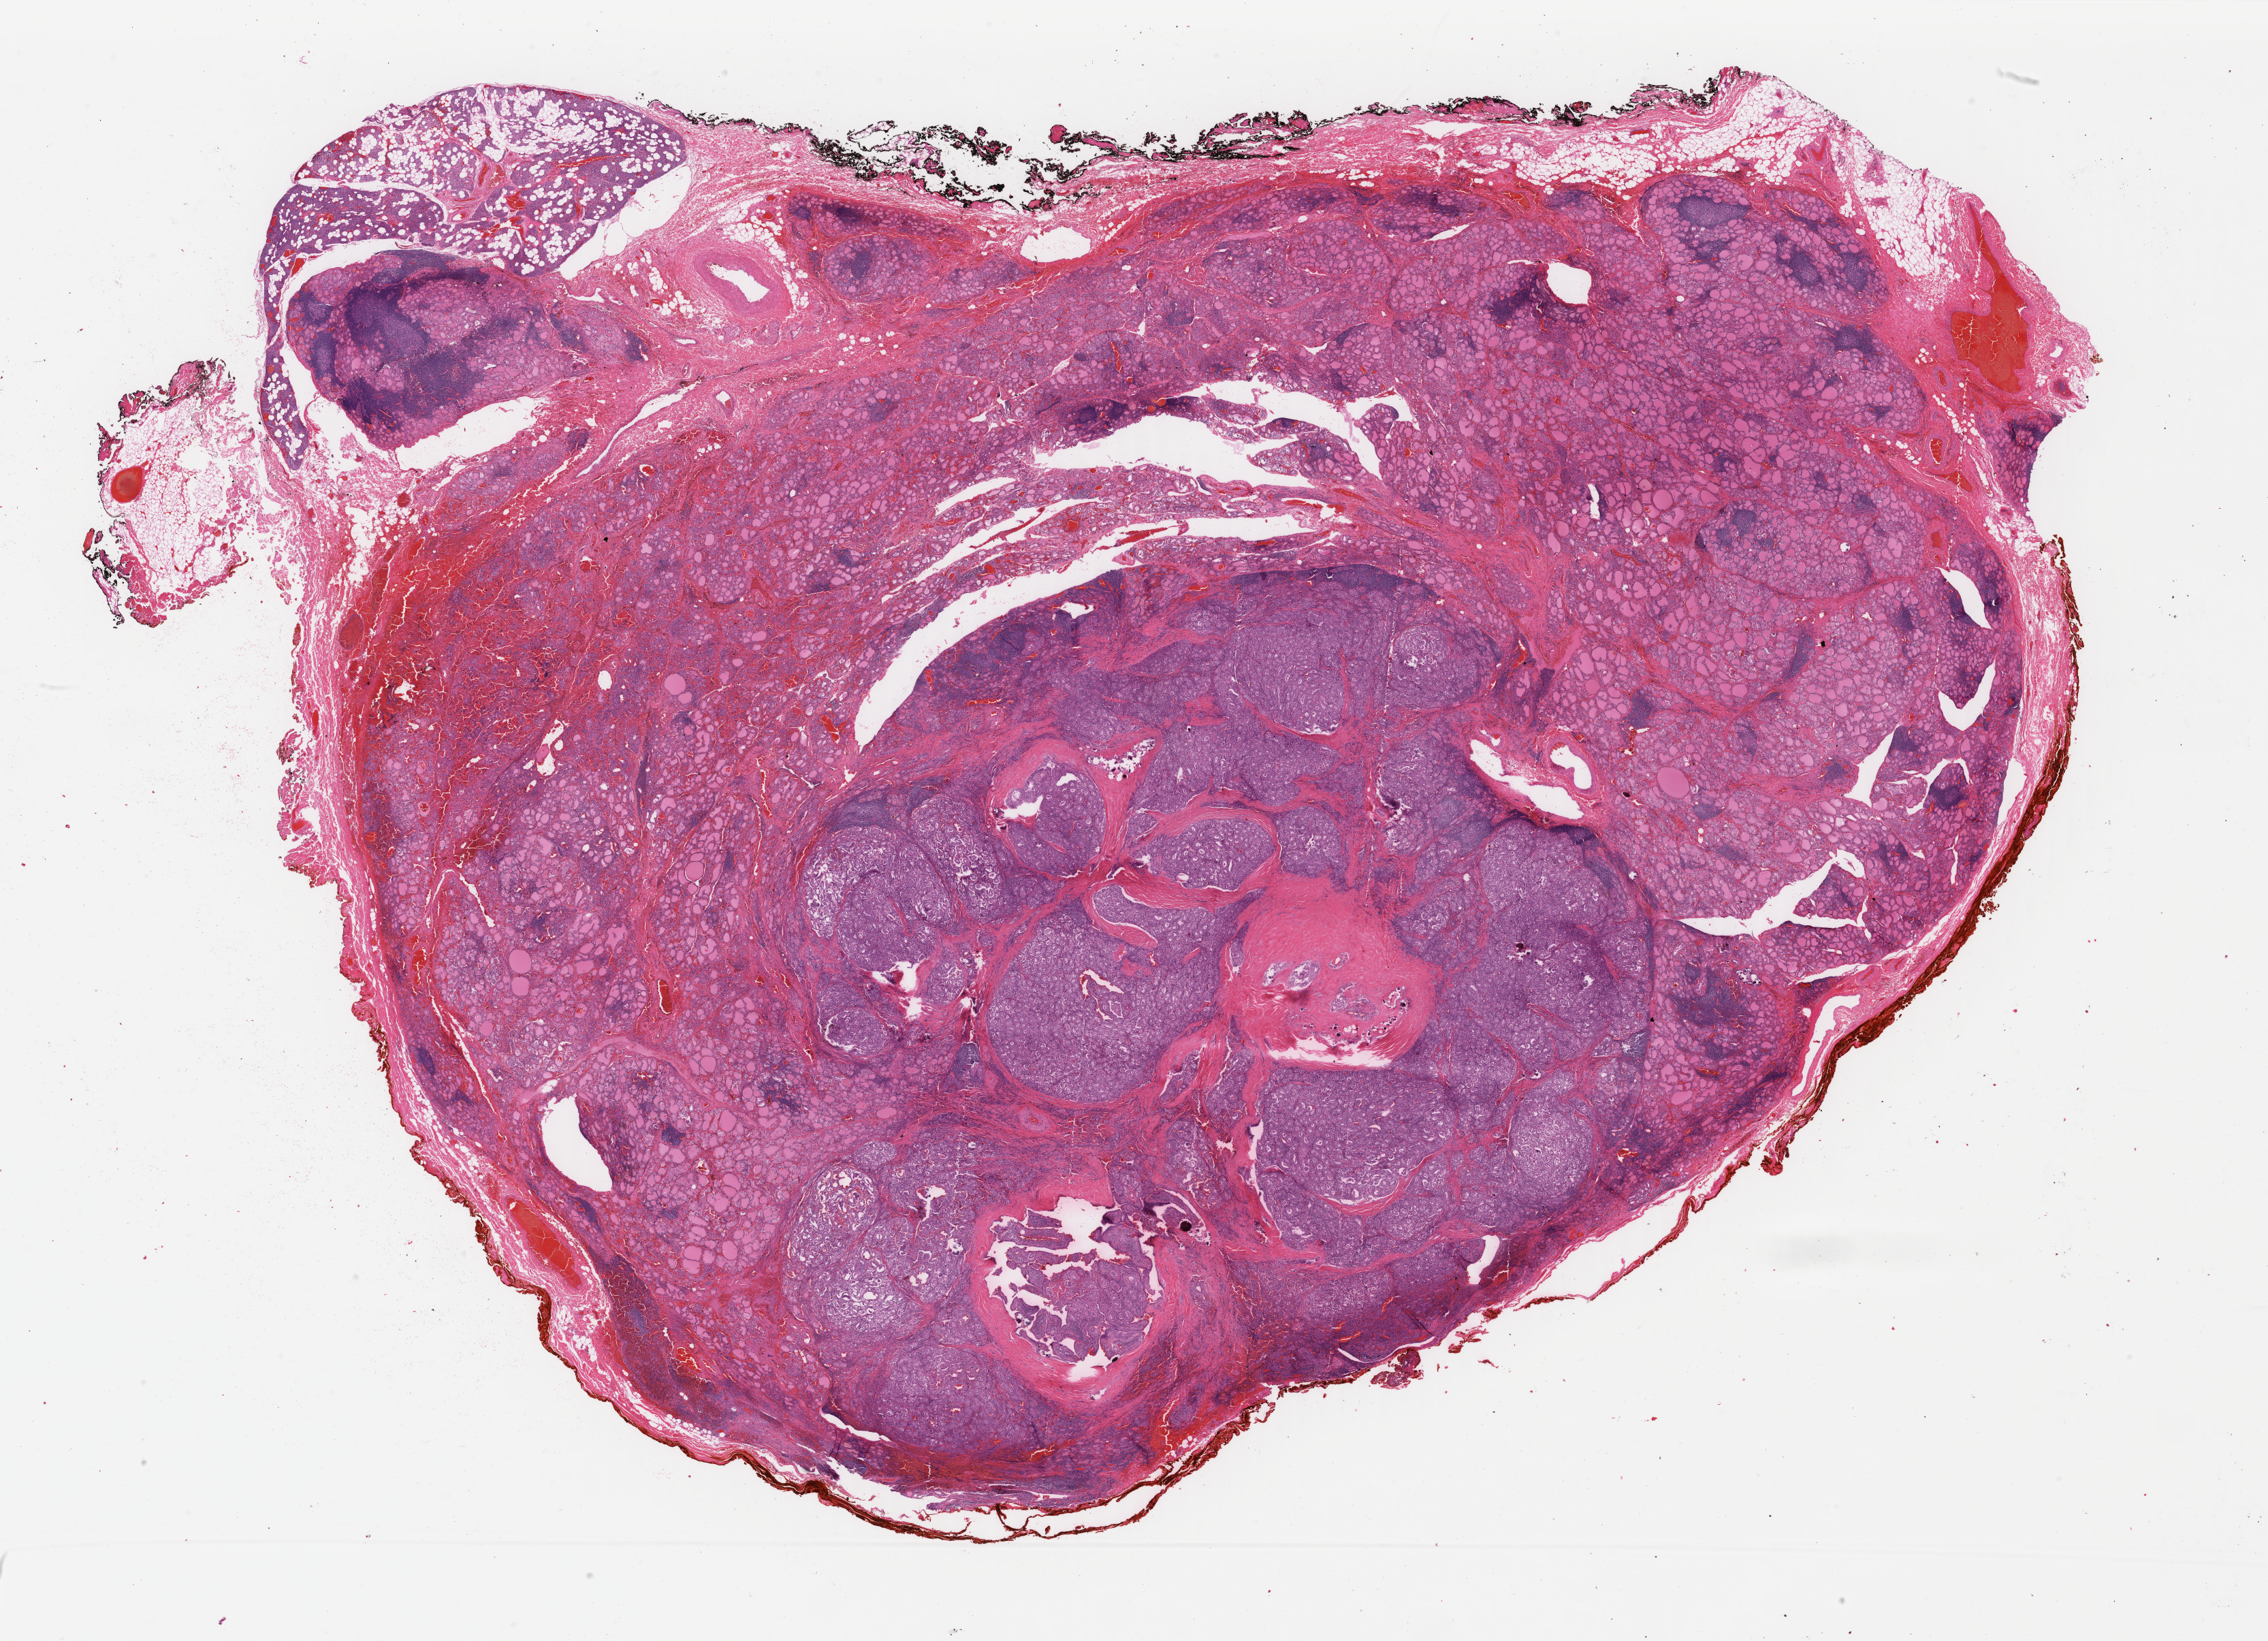
Whole-slide histology image, Hematoxylin and eosin (H&E) stained, low-resolution overview of the scanned area, about 26.4 x 19.1 mm, FFPE section, thyroid, primary tumour sample. Female, age 23 years at initial diagnosis.
AJCC pathologic stage: I. Pathologic diagnosis: Papillary adenocarcinoma, NOS (thyroid gland). Laterality: left.